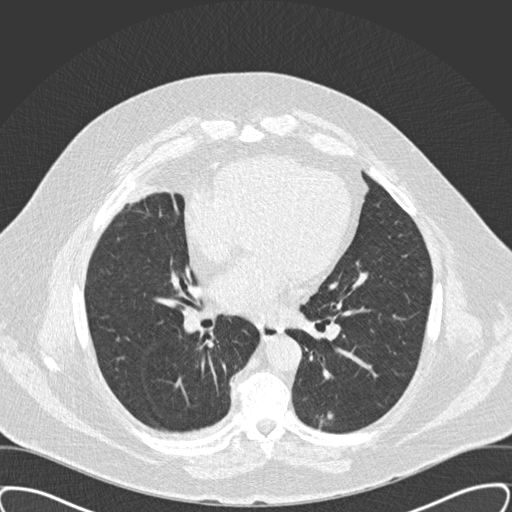
Low-dose screening chest CT, one axial slice; lung window (W 1500 / L -600 HU); 2 mm slice thickness; 512 × 512 image matrix.
Structures marked on this image (manually delineated by an expert):
- lesion 1 (tumor, lower lobe of left lung): bounding box (x1, y1, x2, y2) in pixels: (321, 414, 332, 423)